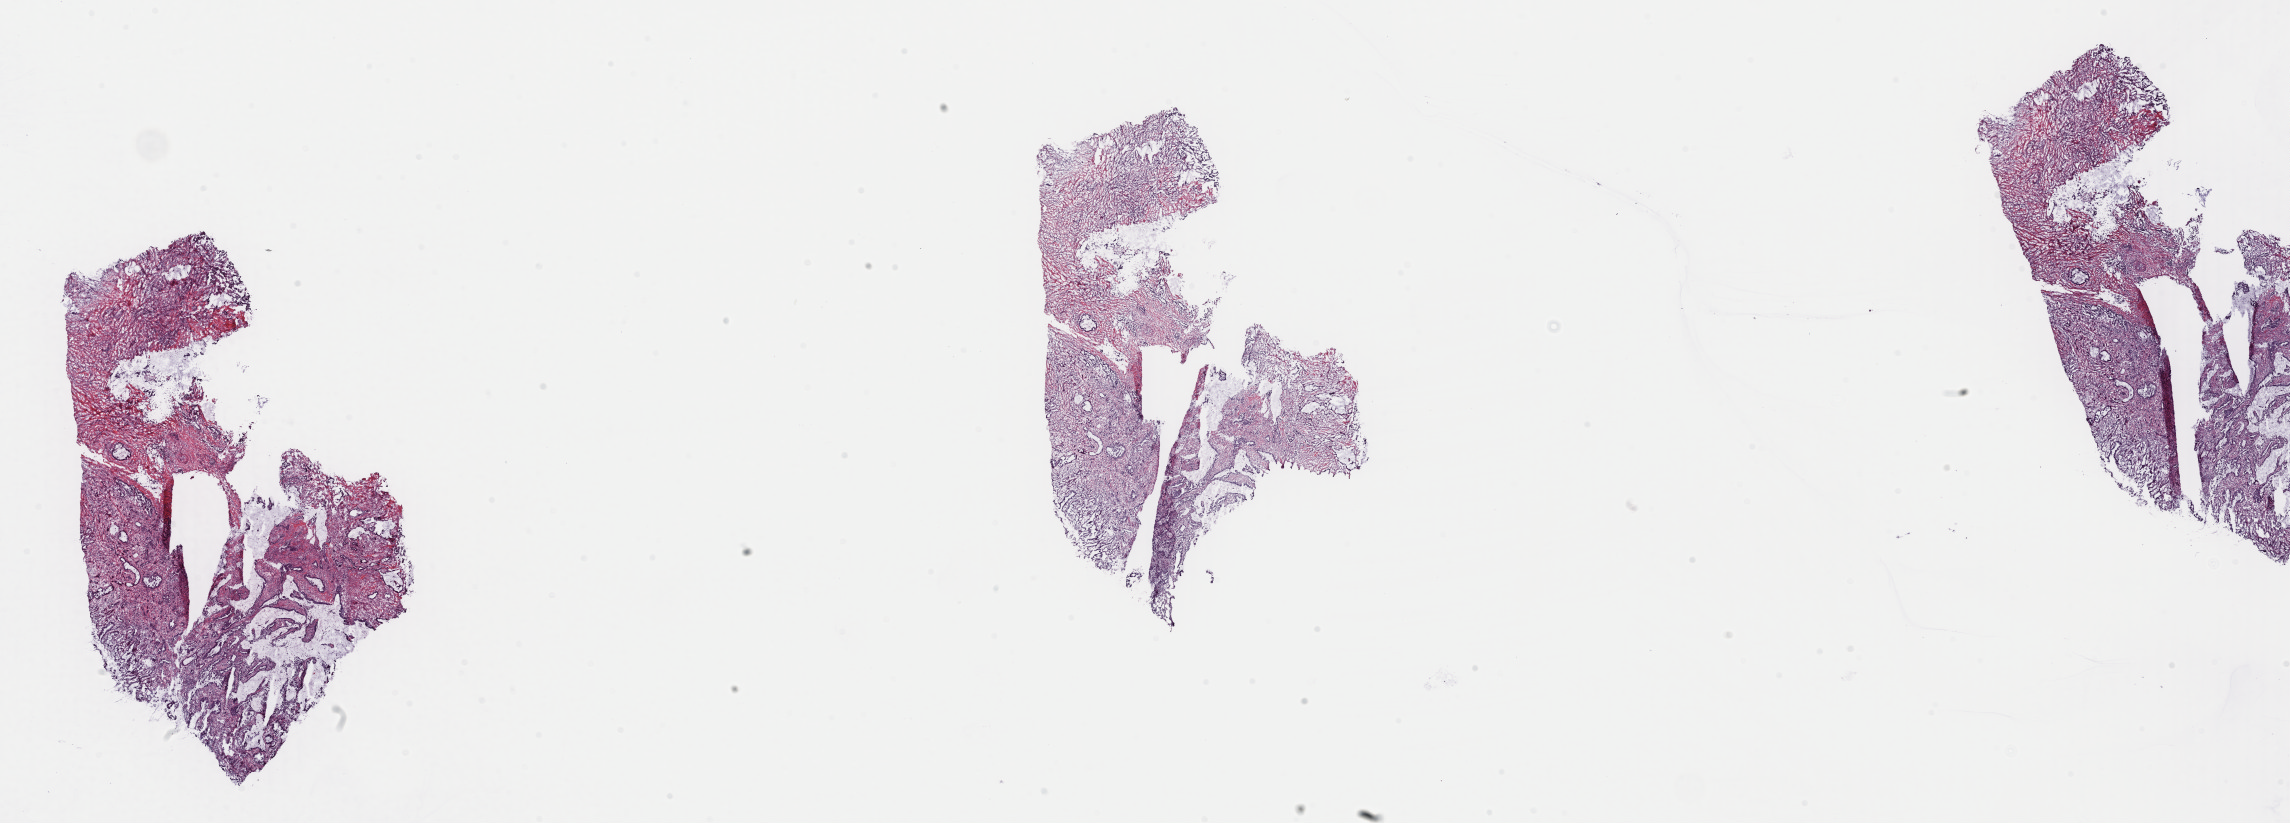
Whole-slide histology image, H&E, shown as a low-resolution overview of the whole scanned area (about 36.1 x 13.0 mm); frozen section from the top of the tissue portion; sample: primary tumour, pancreas. Female, age 65 years at initial diagnosis. Histologic grade: G1 (well differentiated). Pathologist review of this section (percent, as recorded): tumour cells 90%, tumour nuclei 30%, normal cells 0%, stromal cells 10%, necrosis 0%. Infiltration values recorded for this section: lymphocyte infiltration 0%, monocyte infiltration 0%, neutrophil infiltration 0%.
- AJCC pathologic stage: IIB (7th edition)
- histologic diagnosis: Infiltrating duct carcinoma, NOS (head of pancreas)
- lymph nodes positive (case pathology): 2 of 22 examined